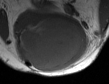
MRI of an extremity soft-tissue mass, one axial slice; slice 24 of 50 in the series (ordered by position); MR volume resampled by the dataset authors to the PET/CT grid (not the native acquisition matrix); 109 × 84 image matrix. Male patient. Case-level facts recorded for this patient, not image findings: histological type: synovial sarcoma; site of the primary tumour: left poplietal fossa.
Annotated regions visible in this slice (expert contour drawn on MRI and transferred to this co-registered scan by the dataset authors):
- gross tumour volume (mass): bounding box <16,14,88,72> (left, top, right, bottom; pixels)